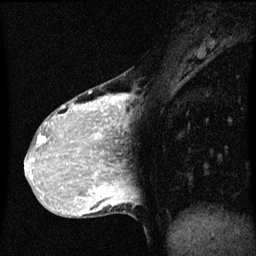
Breast MRI (dynamic contrast-enhanced), one sagittal slice; dynamic contrast-enhanced series, image 2 of 3 at this slice position (ordered by acquisition); 1.5 T; TE 4.2 ms, TR 8 ms; 2 mm slice thickness; 256 × 256 image matrix, field of view 200 × 200 mm. Patient: female, 36 years.
Outlined on this slice (semi-automatically segmented with operator editing):
- analysis volume of interest (the breast-tissue region the enhancement analysis was run in; not a lesion): box from (x=33, y=74) to (x=124, y=169) px
- tumour enhancement mask (voxels above the 70 % enhancement threshold inside the analysis volume of interest): (x=33, y=96)–(x=121, y=169)